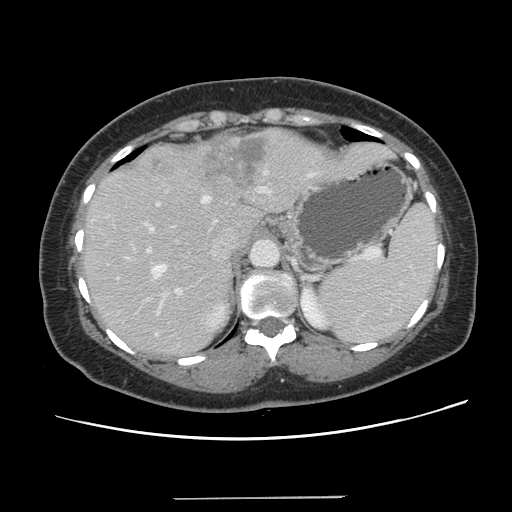
Contrast-enhanced abdominal CT, one axial slice; position 96 of 141 along the scan axis; intravenous contrast given; soft-tissue window (W 400 / L 40 HU); 512 × 512 image matrix, field of view 366 × 366 mm. Female patient, age 53 years. From the clinical record (not read from this slice): diagnosis: colorectal cancer liver metastases, imaged before liver resection; multiple liver metastases: no.
Annotated regions visible in this slice (expert manual segmentation):
- hepatic veins: bounding box <151,170,316,277> (left, top, right, bottom; pixels)
- liver: <84,129,392,355>
- planned liver remnant (the part of the liver to remain after resection): <84,210,261,355>
- portal vein (with intrahepatic branches): <143,187,265,316>
- liver metastasis: <195,136,267,189>